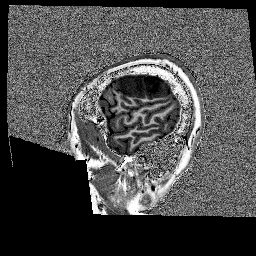
Brain MRI from a brain-tumour surgery series, one sagittal slice. Slice 31 of 176 in the series (ordered by position). 1 mm slice thickness. 256 × 256 image matrix. Case-level facts recorded for this patient, not image findings: histopathology: Glioblastoma; WHO grade: 4; IDH mutation: no; tumour location: Left Frontal.
Structures marked on this image (manually delineated by an expert):
- tumour: bounding box [x1, y1, x2, y2] px = [118, 74, 175, 98]